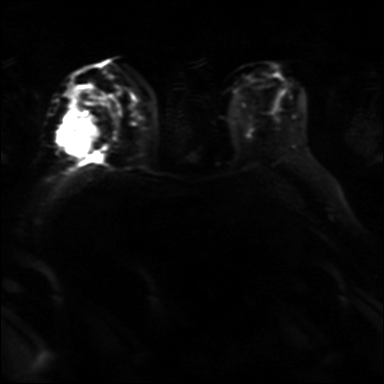
Breast MRI, one axial slice; slice 20 of 36 in the series (ordered by position); diffusion-weighted series; image 2 of 4 stored at this slice position (different b-values; order by instance number); 3 T; 4 mm slice thickness; 384 × 384 image matrix, field of view 320 × 320 mm. Female patient.
Structures marked on this image (manually delineated by an expert):
- tumour on diffusion-weighted imaging: box from (x=59, y=115) to (x=97, y=154) px